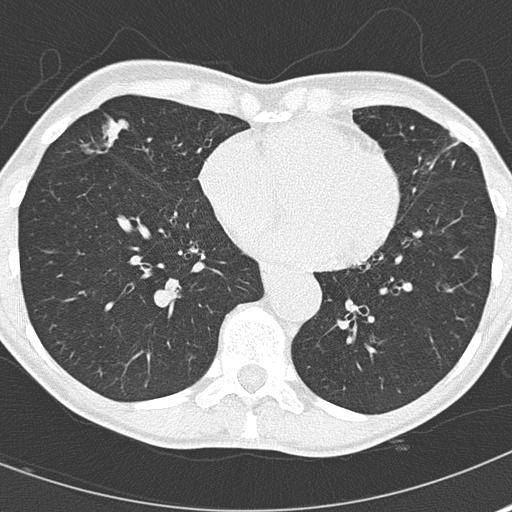
Axial slice from a low-dose chest CT screening exam, second annual screen, lung window (W 1500 / L -600 HU), 2 mm slice thickness, lung (sharp) reconstruction kernel (B50f), slice 109 of 167 in the series. Female participant, aged 67 years at enrolment.
- Lesion marked by an expert reader, bounding box [x1, y1, x2, y2] px = [84, 105, 193, 195].
- The screening reader recorded 2 non-calcified nodules or masses ≥4 mm on this exam; which of them this box marks is not recorded.
- Official screen result: positive, other.
- Participant outcome: lung cancer diagnosed 475 days after this screen (after the third annual screen) — bronchiolo-alveolar adenocarcinoma, NOS, right middle lobe, well differentiated (G1), stage IA (AJCC 6th edition), 25 mm at pathology.